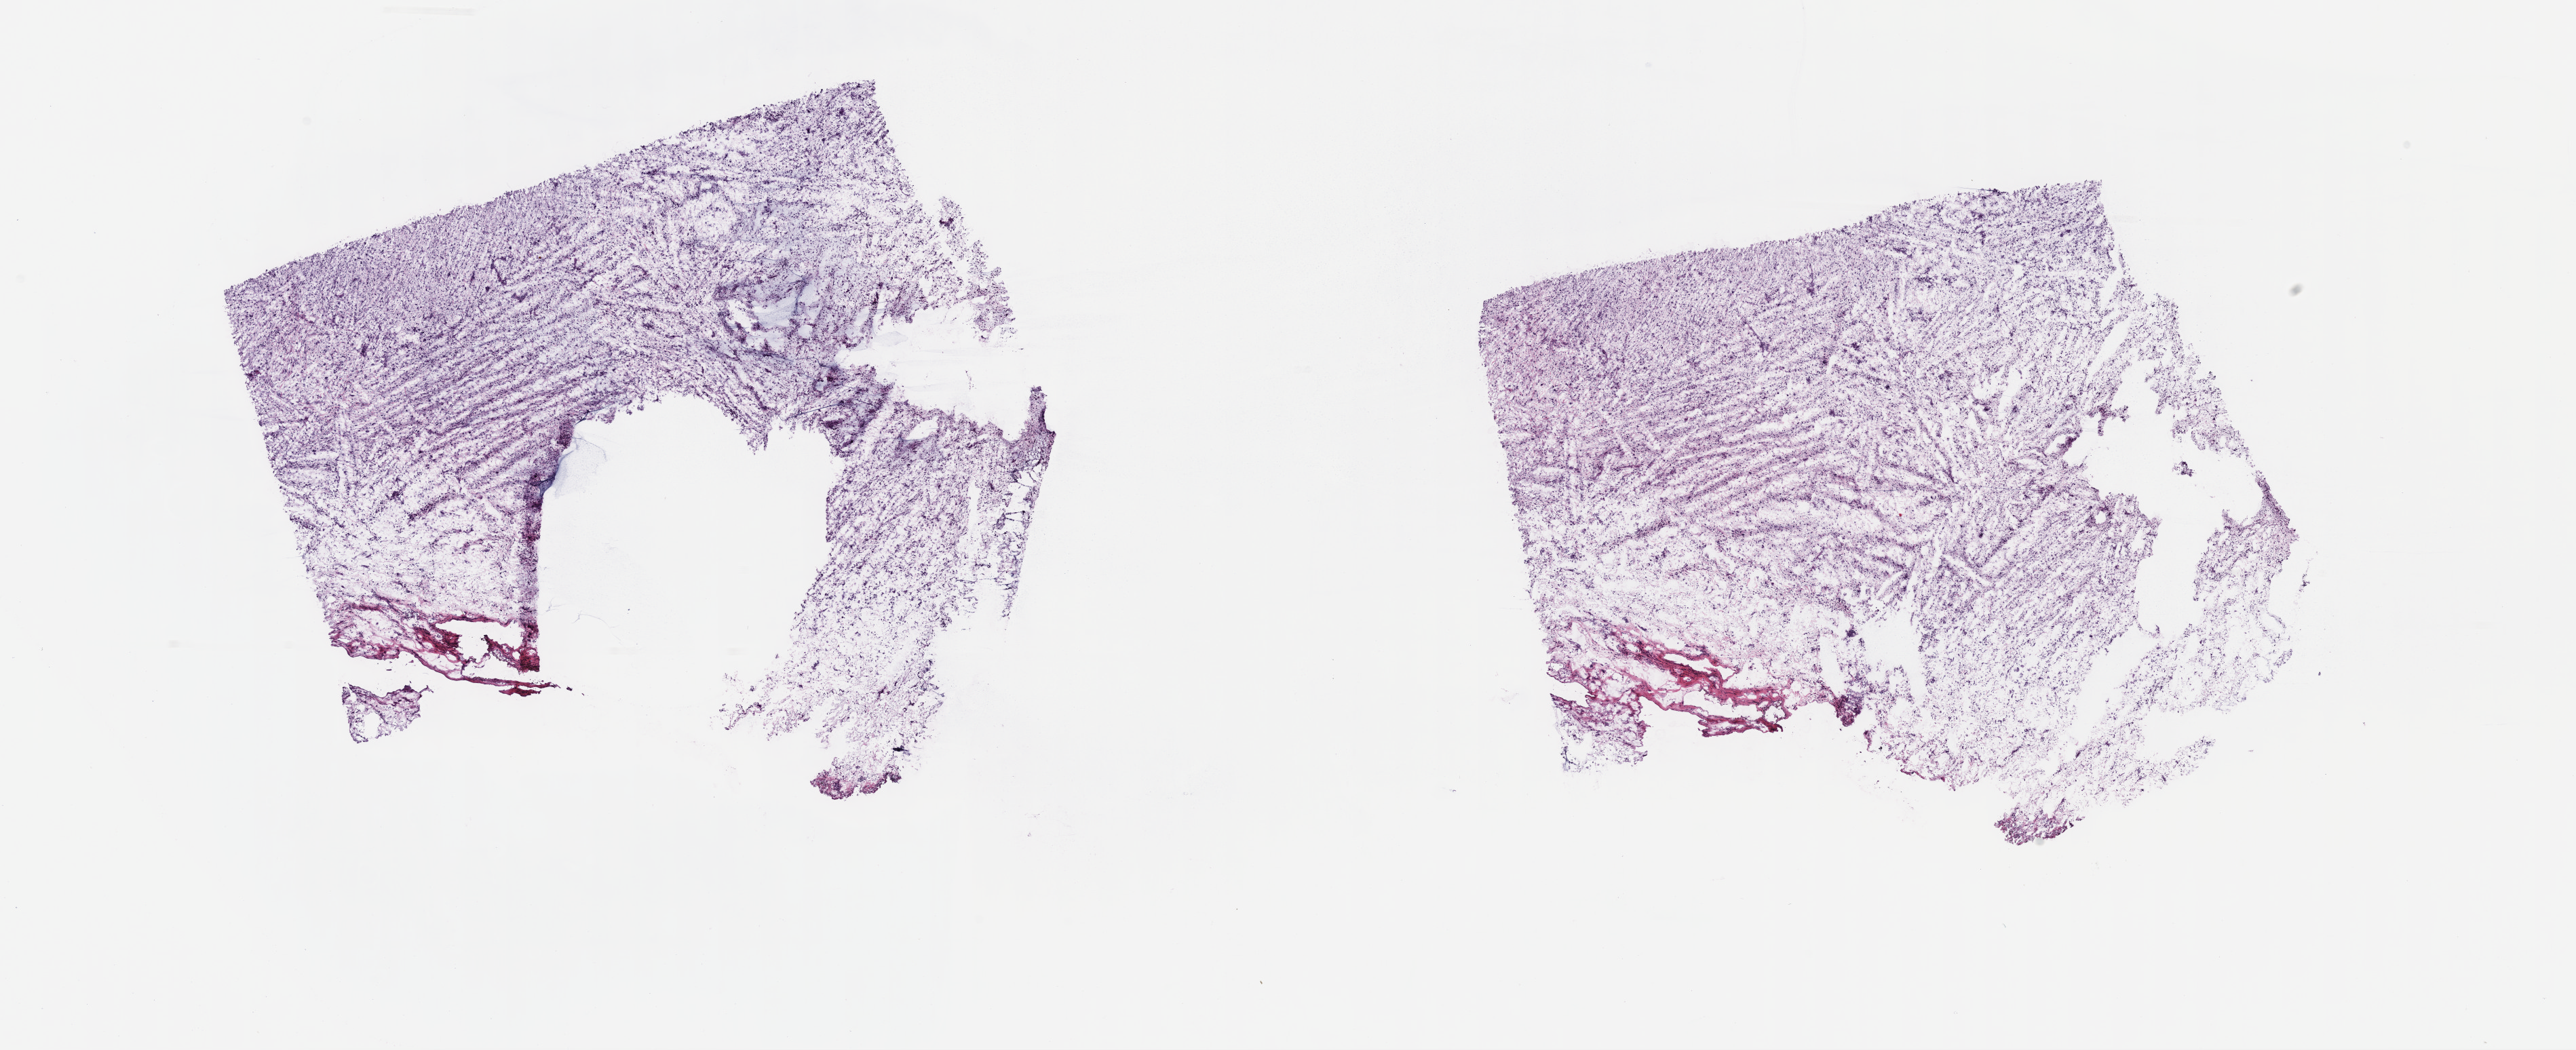
H&E whole-slide image, shown as a low-resolution overview of the whole scanned area (about 30.7 x 12.5 mm, acquisition: 40x scan), frozen section, primary tumour sample from the connective, subcutaneous and other soft tissues. Patient: female, age at initial diagnosis 83 years. Composition of this section per pathologist review: tumour cells 90%, tumour nuclei 95%, normal cells 0%, stromal cells 10%, necrosis 0%. Inflammatory infiltration, as recorded: lymphocyte infiltration 0%, monocyte infiltration 0%, neutrophil infiltration 0%.
Diagnosis: Fibromyxosarcoma.